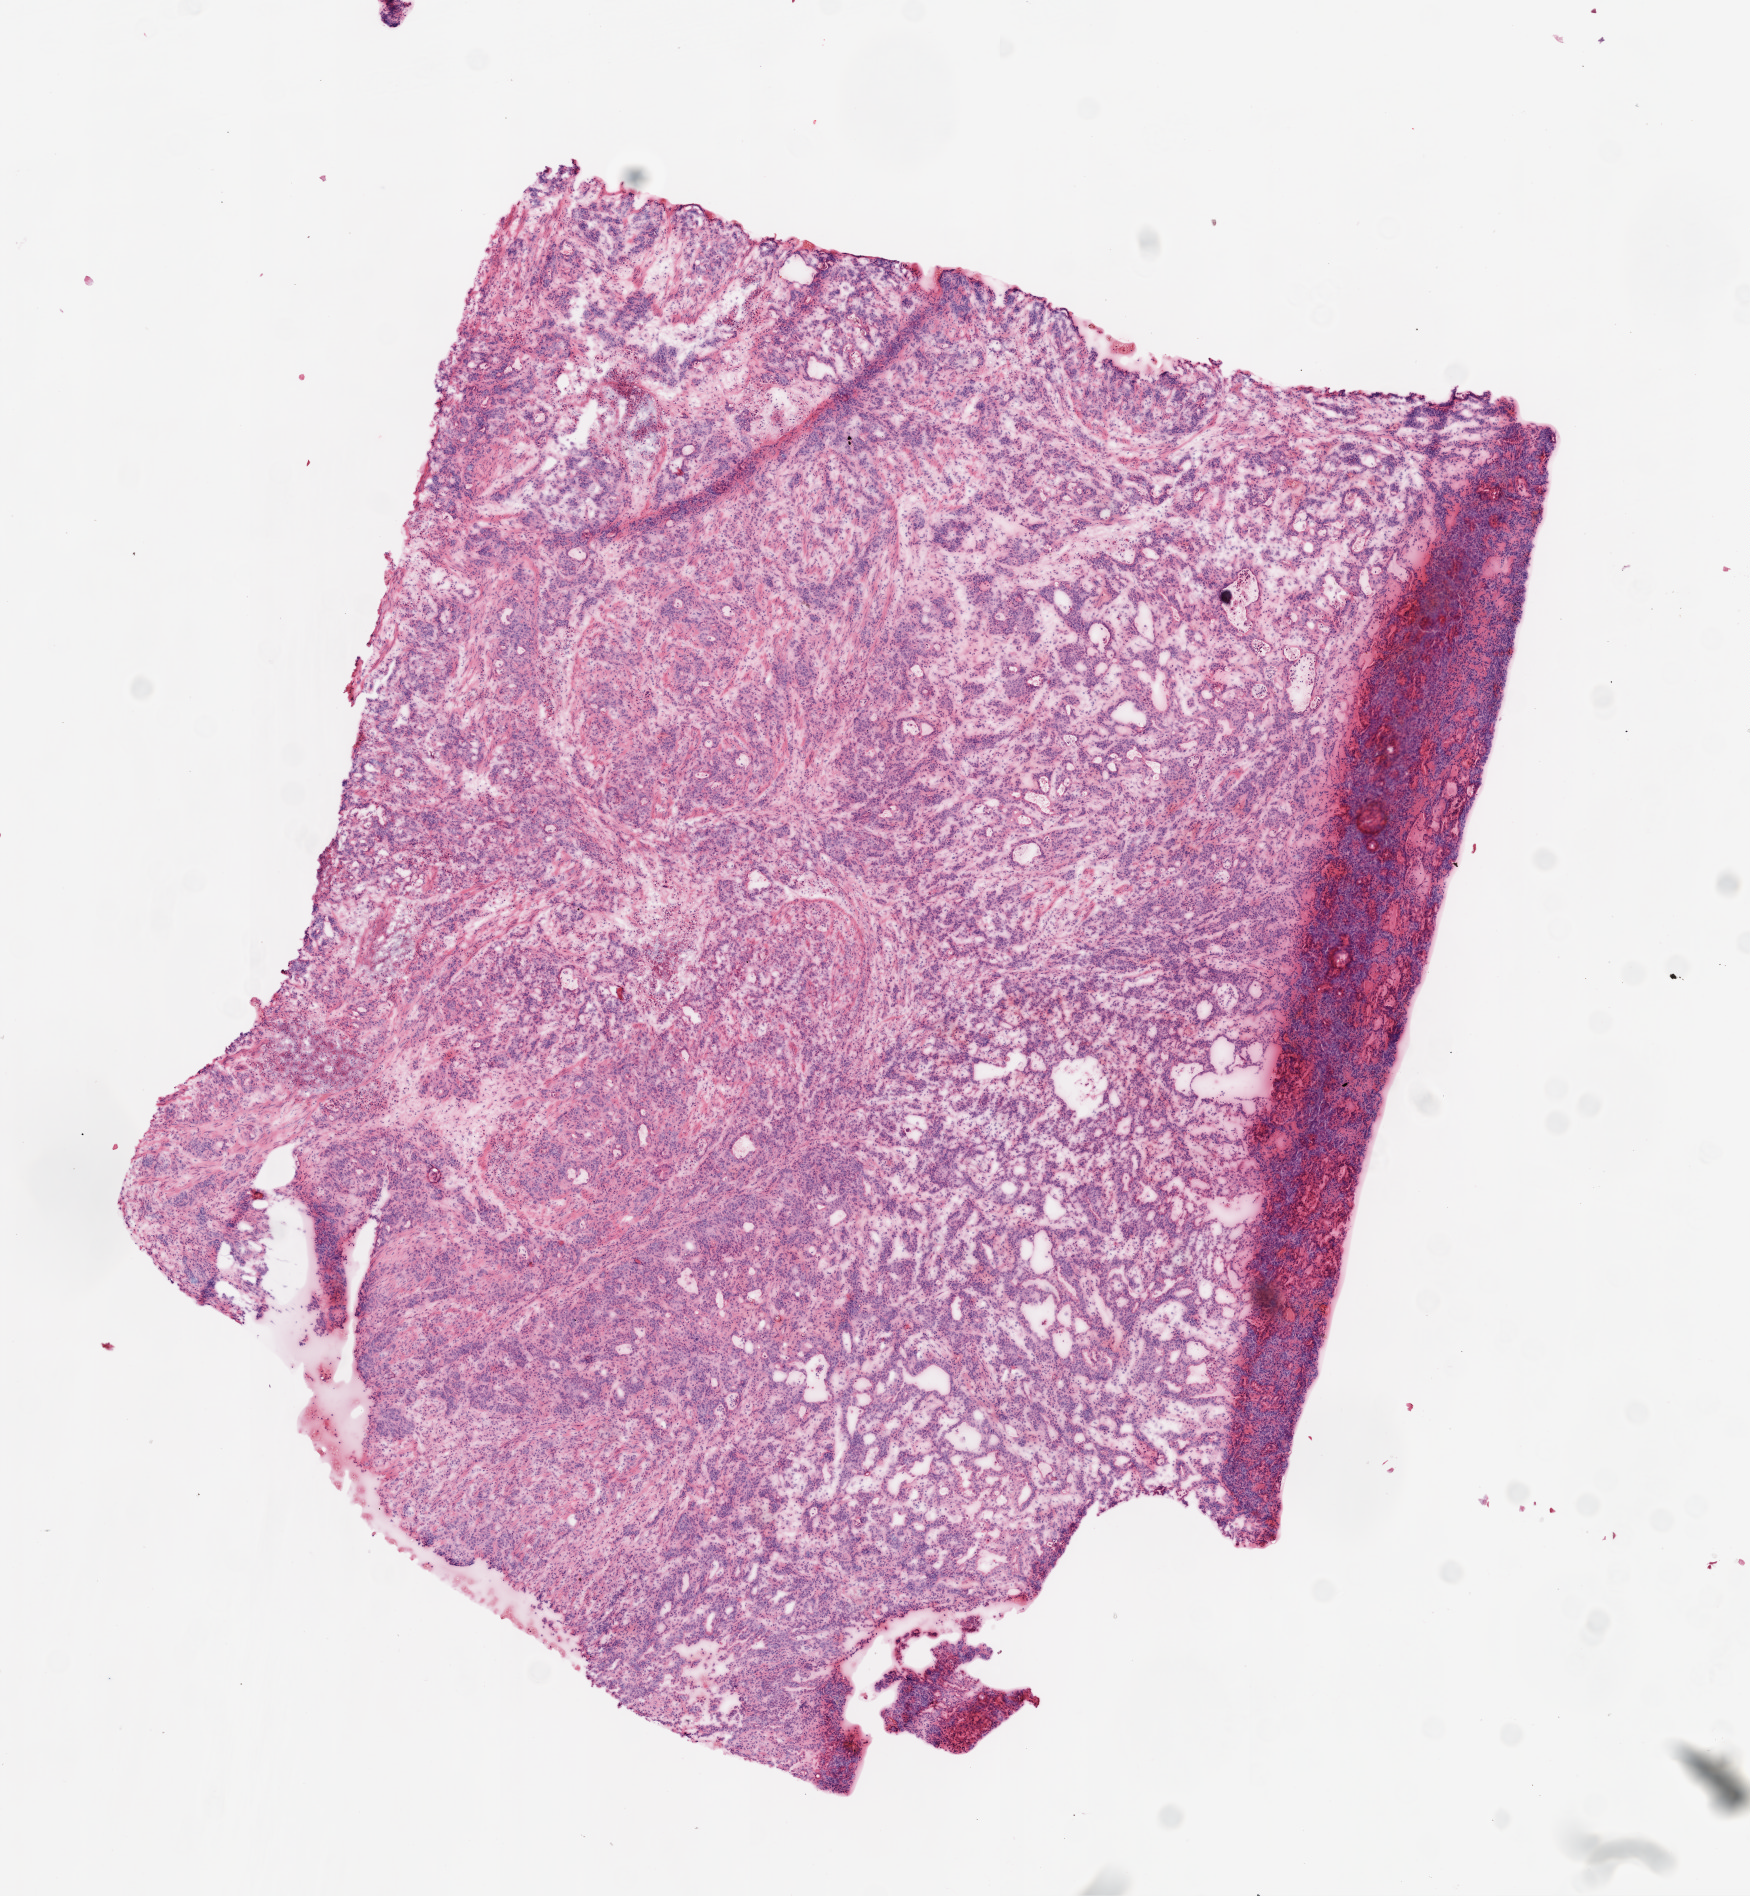
Digitized H&E-stained tissue section (whole slide) — whole scanned area (about 7.0 x 7.6 mm, slide scanned at 20x) shown as a low-resolution overview, frozen section from the top of the tissue portion, stomach, primary tumour sample. Female patient; age at initial diagnosis 53 years. Histologic grade: G2 (moderately differentiated). Composition of this section per pathologist review: tumour cells 80%, tumour nuclei 80%, normal cells 0%, stromal cells 20%, necrosis 0%.
TNM: T2 N3 M0. Lymph nodes positive (case pathology): 19 of 34 examined. AJCC pathologic stage: IIIA (7th edition). Diagnosis: Tubular adenocarcinoma.